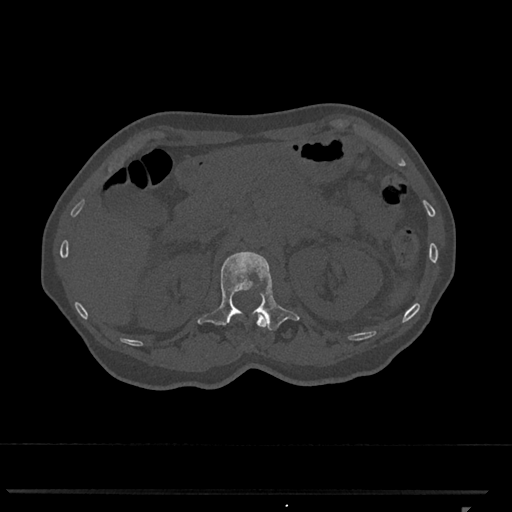
CT including the spine, one axial slice. Bone window (W 1800 / L 400 HU). 0.5 mm slice thickness. 512 × 512 image matrix. Patient: female, 62 years. Case-level facts recorded for this patient, not image findings: primary cancer: renal.
Structures marked on this image (semi-automatic segmentation, software-assisted and operator-edited):
- L1 vertebra: box from (x=197, y=251) to (x=300, y=330) px
- T12 vertebra: (x=256, y=315)–(x=266, y=327)